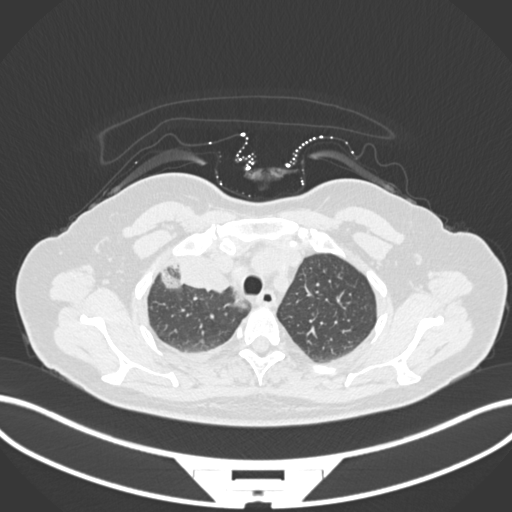
Chest CT, one axial slice; position 136 of 172 along the scan axis; reconstruction kernel B30f; lung window (W 1500 / L -600 HU); 1 mm slice thickness; 512 × 512 image matrix, field of view 400 × 400 mm. Female patient, age 52 years. Case-level facts recorded for this patient, not image findings: clinical TNM (as recorded): T3 N1 M1.
Structures marked on this image (rectangle marked by the reading radiologist):
- lung tumour (recorded histology: adenocarcinoma): bounding box [x1, y1, x2, y2] px = [155, 254, 237, 295]